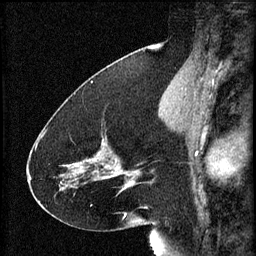
Breast MRI (dynamic contrast-enhanced), one sagittal slice. Position 28 of 60 along the scan axis. 3 images stored at this slice position (order not interpretable as contrast timing). 1.5 T. TE 4.2 ms, TR 8.2 ms. 256 × 256 image matrix, field of view 180 × 180 mm. Patient: female, 41 years.
Annotated regions visible in this slice (semi-automatically segmented with operator editing):
- analysis volume of interest (the breast-tissue region the enhancement analysis was run in; not a lesion): bounding box <72,124,134,195> (left, top, right, bottom; pixels)
- tumour enhancement mask (voxels above the 70 % enhancement threshold inside the analysis volume of interest): <75,148,134,189>